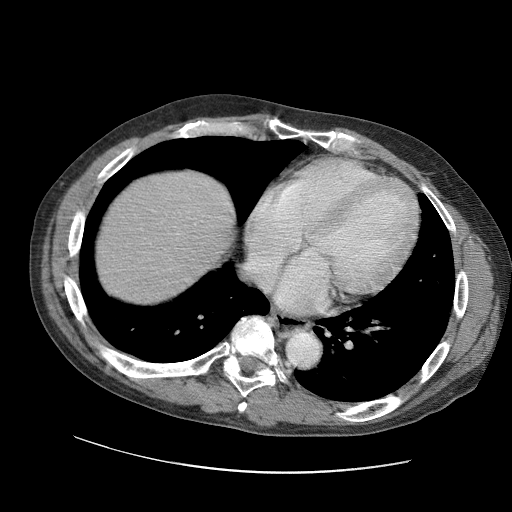
Contrast-enhanced abdominal CT (liver protocol), one axial slice. Slice 93 of 109 in the series (ordered by position). Soft-tissue window (W 400 / L 40 HU). 2.5 mm slice thickness. 512 × 512 image matrix, field of view 400 × 400 mm. Case-level facts recorded for this patient, not image findings: diagnosis: hepatocellular carcinoma (patient treated with transarterial chemoembolisation; whether this scan precedes or follows treatment is not stated here); TNM stage (as recorded): Stage-IIIC; Child-Pugh class: B; tumour differentiation: well differentiated; tumour nodularity: uninodular.
Annotated regions visible in this slice (semi-automatic segmentation, software-assisted and operator-edited):
- liver parenchyma outside the tumour (the mass and vessels are separate outlines, so this box may not span the whole liver): bounding box <94,170,234,304> (left, top, right, bottom; pixels)
- liver vessels: <148,220,211,253>